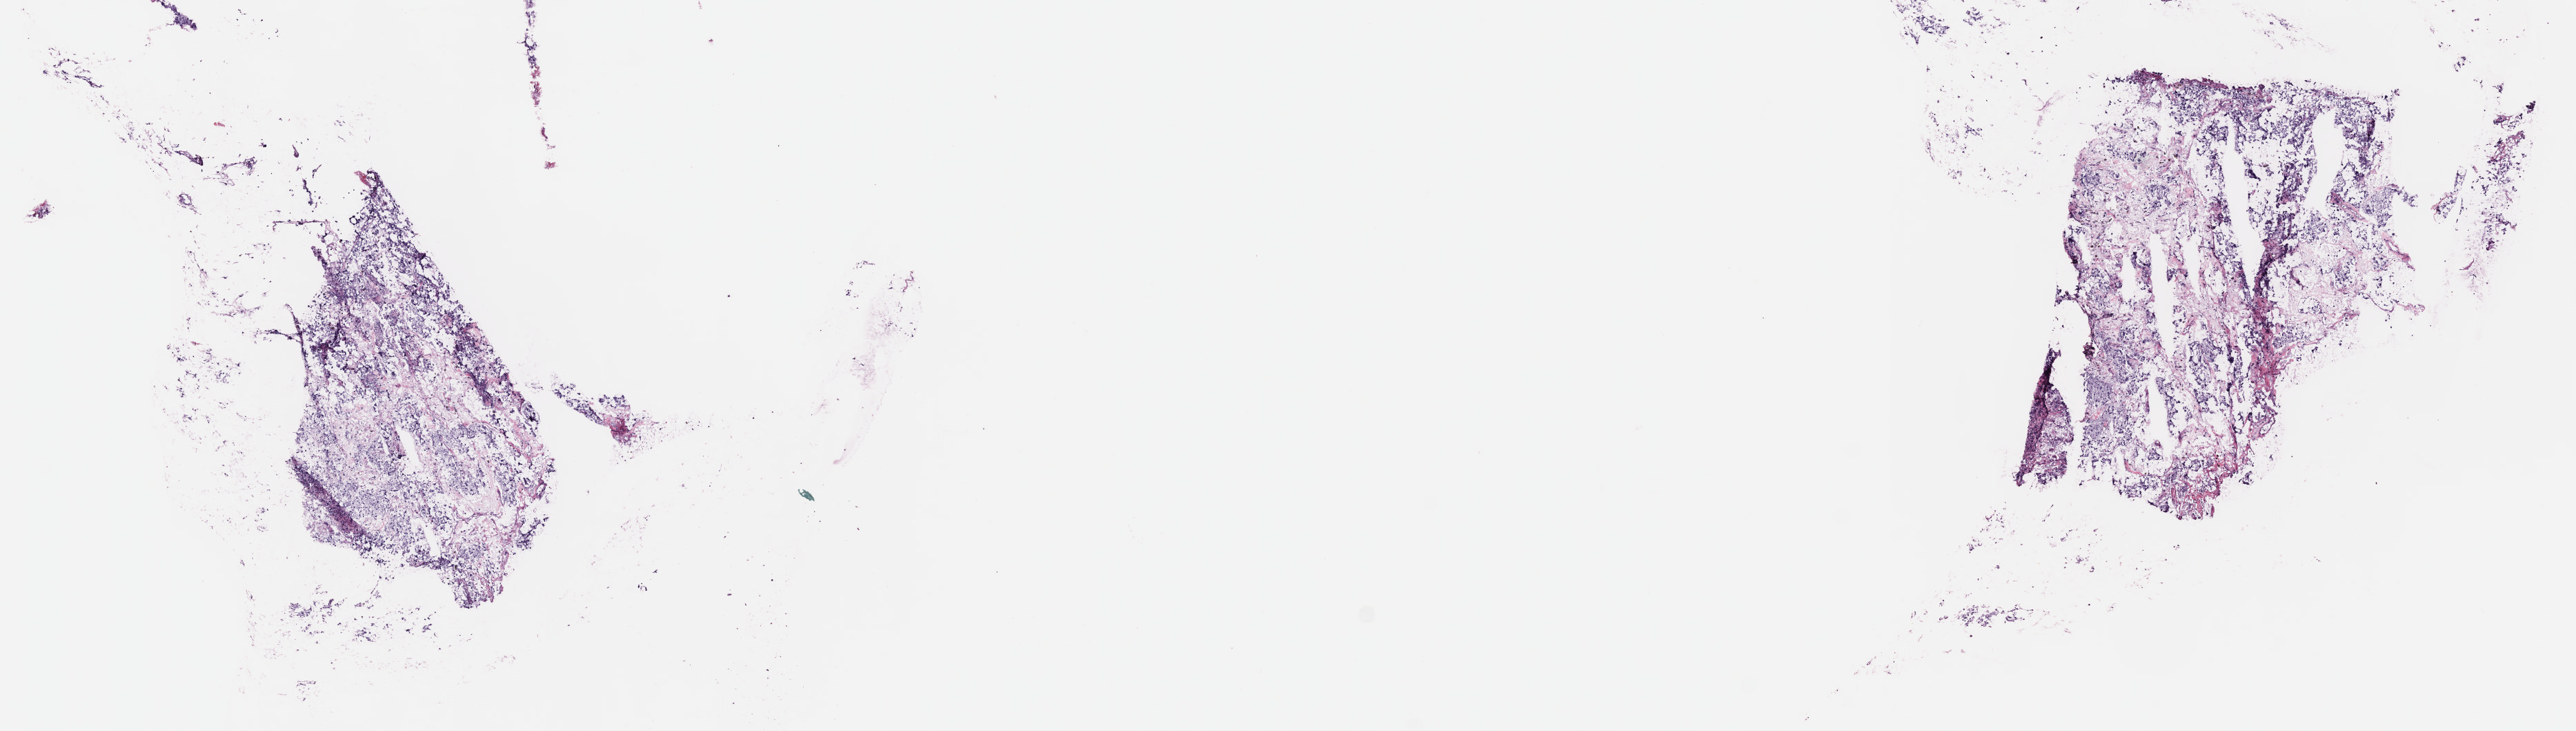
Hematoxylin and eosin (H&E) stained whole-slide image — low-resolution overview of the scanned area, about 15.1 x 4.3 mm (slide scanned at 40x); frozen section from the top of the tissue portion; adrenal gland, primary tumour sample. Male patient; age at initial diagnosis 67 years. Slide review estimates, as recorded: tumour cells 70%, tumour nuclei 70%.
Diagnosis: Pheochromocytoma, NOS.